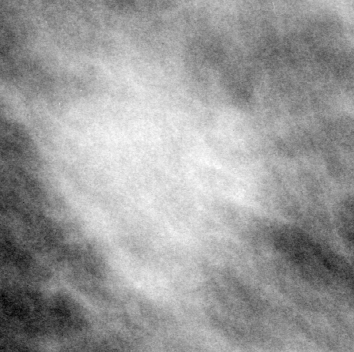
Crop from a digitized film mammogram around one marked abnormality, left breast, MLO view.
Finding: mass, shape oval, margins microlobulated; BI-RADS assessment category 4; subtlety rating 5 on a 1 (subtle) to 5 (obvious) scale; pathology (as recorded): malignant.